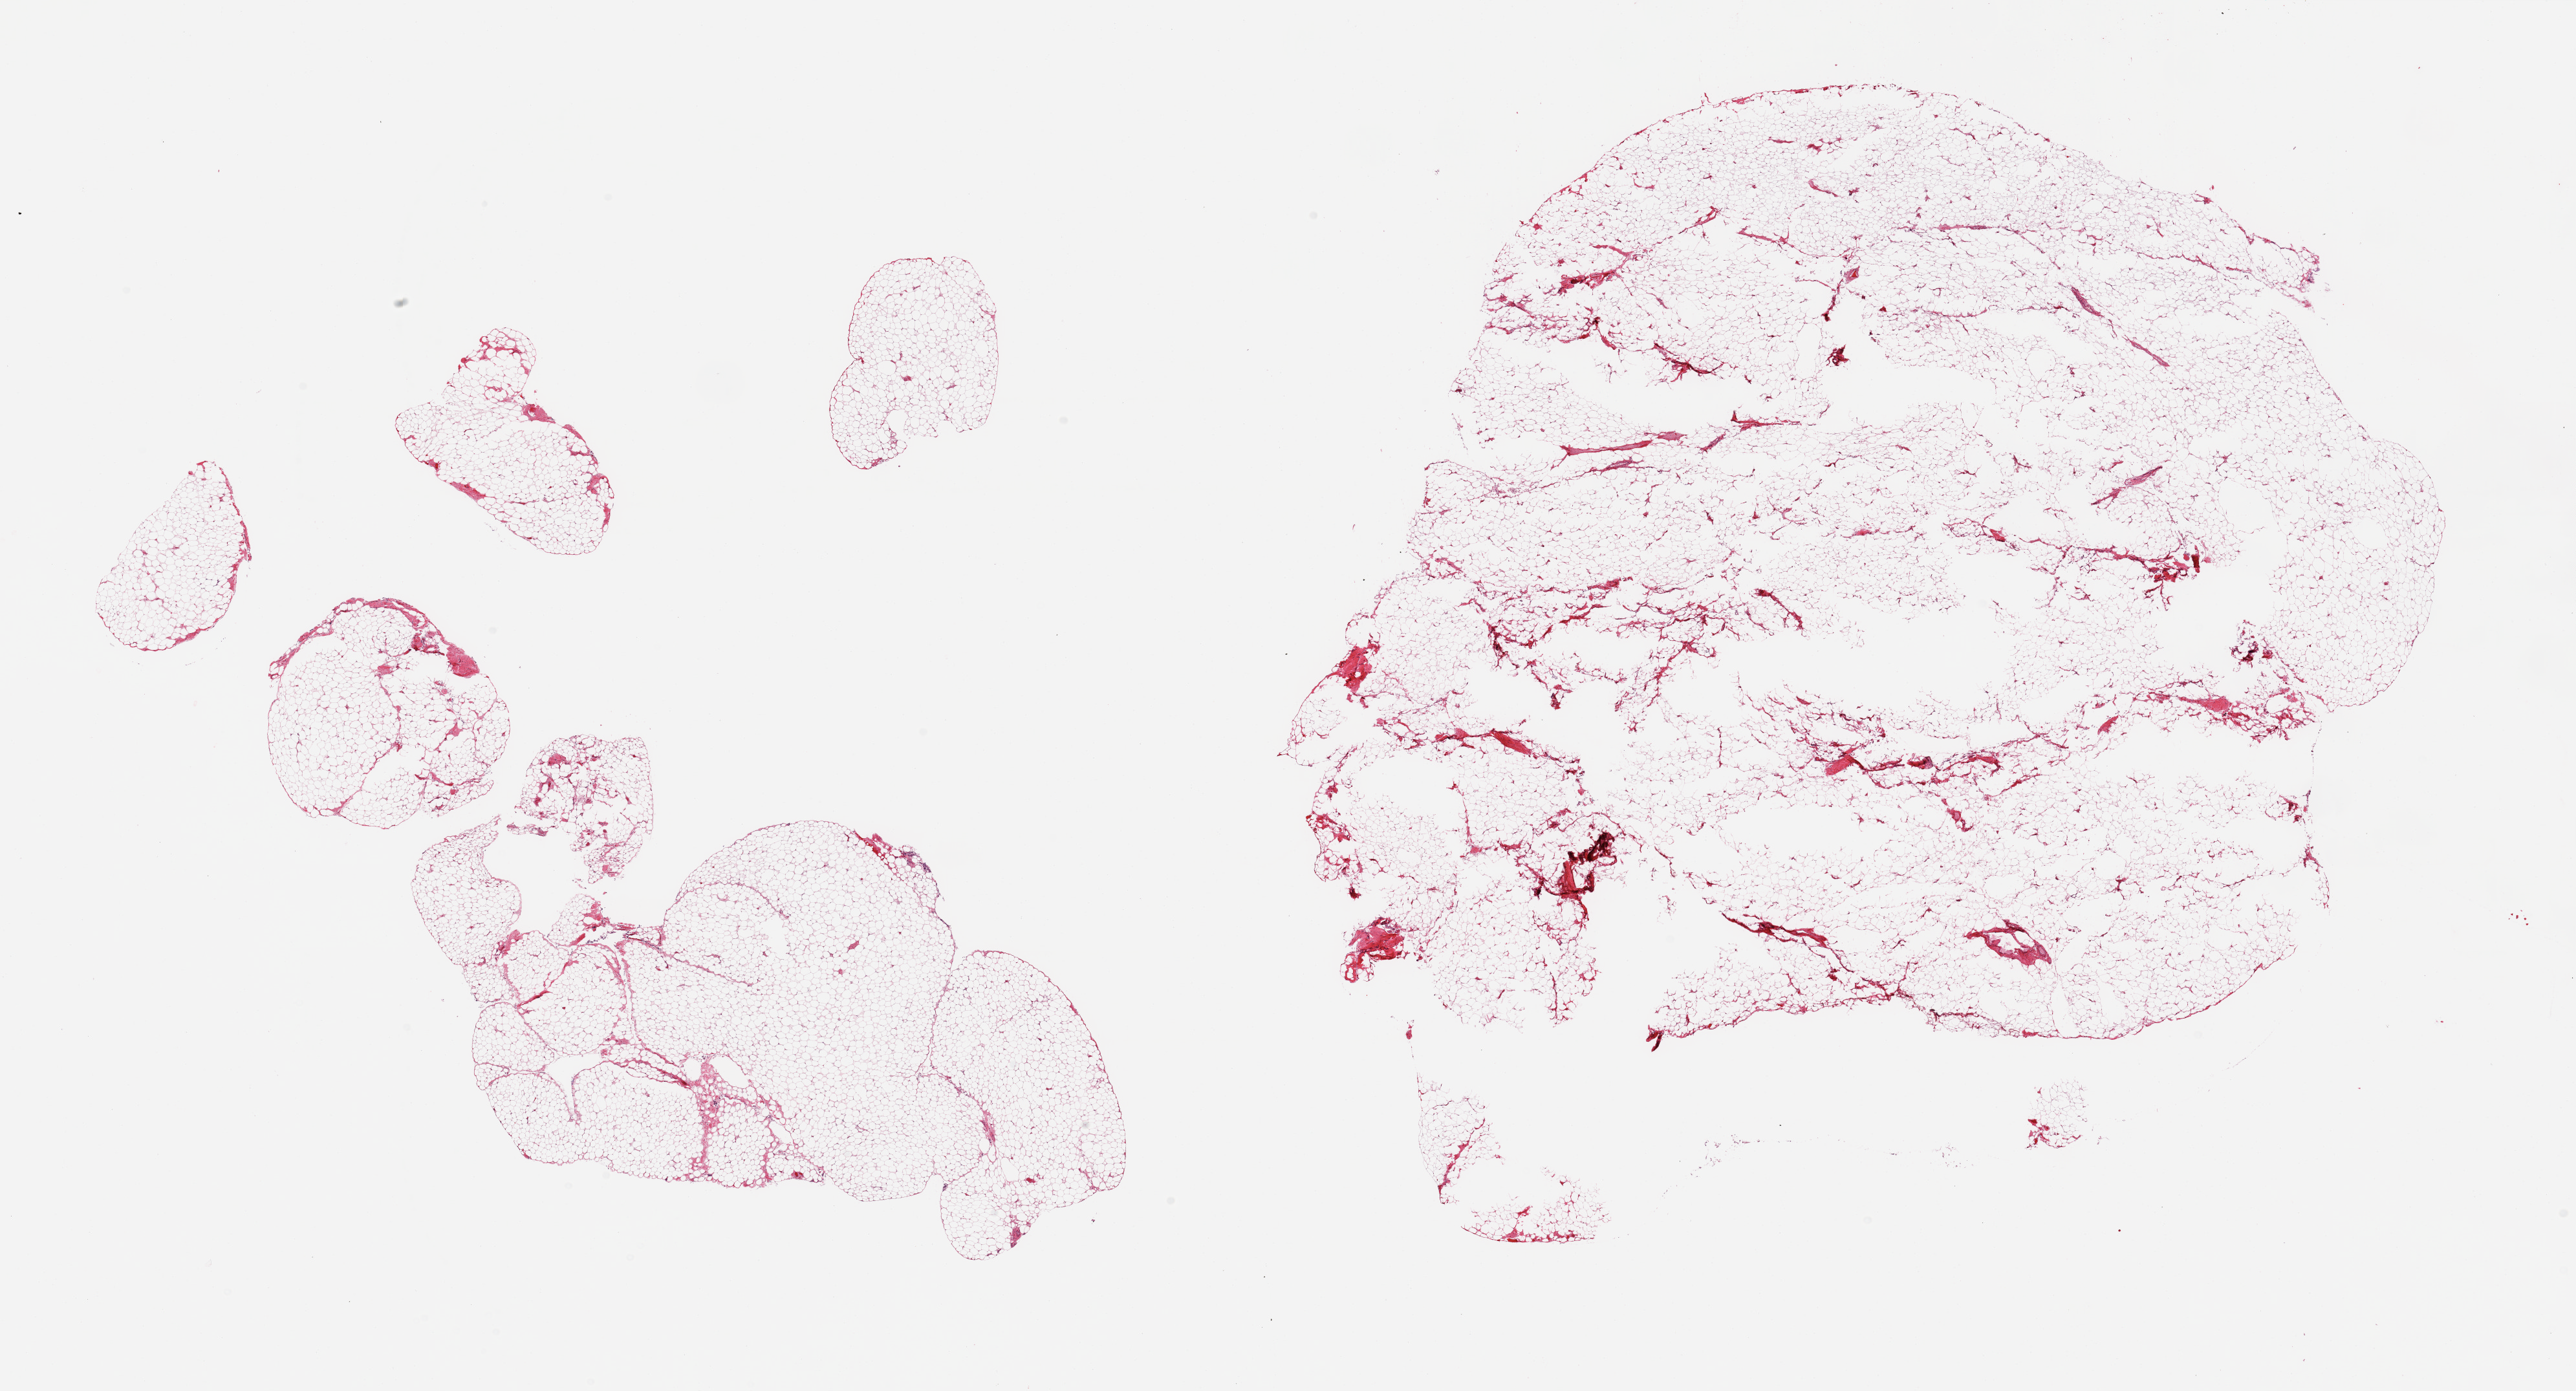
H&E whole-slide image — a low-resolution overview of the entire scanned area, about 31.5 x 17.0 mm, PAXgene-fixed, paraffin-embedded tissue, section of omentum (target tissue), tissue donor sample. Donor sex: male.
Pathologist's review note for this sample: 2 pieces; some defects in tissue (oversized).